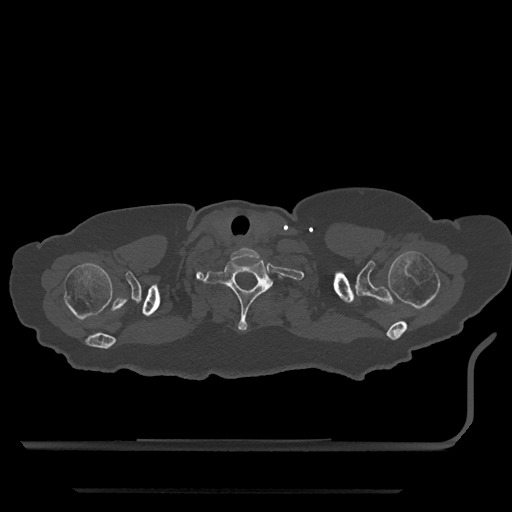
CT including the spine, one axial slice. Slice 711 of 797 in the series (ordered by position). Bone window (W 1800 / L 400 HU). 0.5 mm slice thickness. 512 × 512 image matrix. Female patient, age 51 years. Case-level facts recorded for this patient, not image findings: primary cancer: neuro; vertebrae with lytic lesions (as recorded): T8.
Outlined on this slice (semi-automatically segmented with operator editing):
- T1 vertebra: bounding box (x1, y1, x2, y2) in pixels: (204, 260, 283, 331)